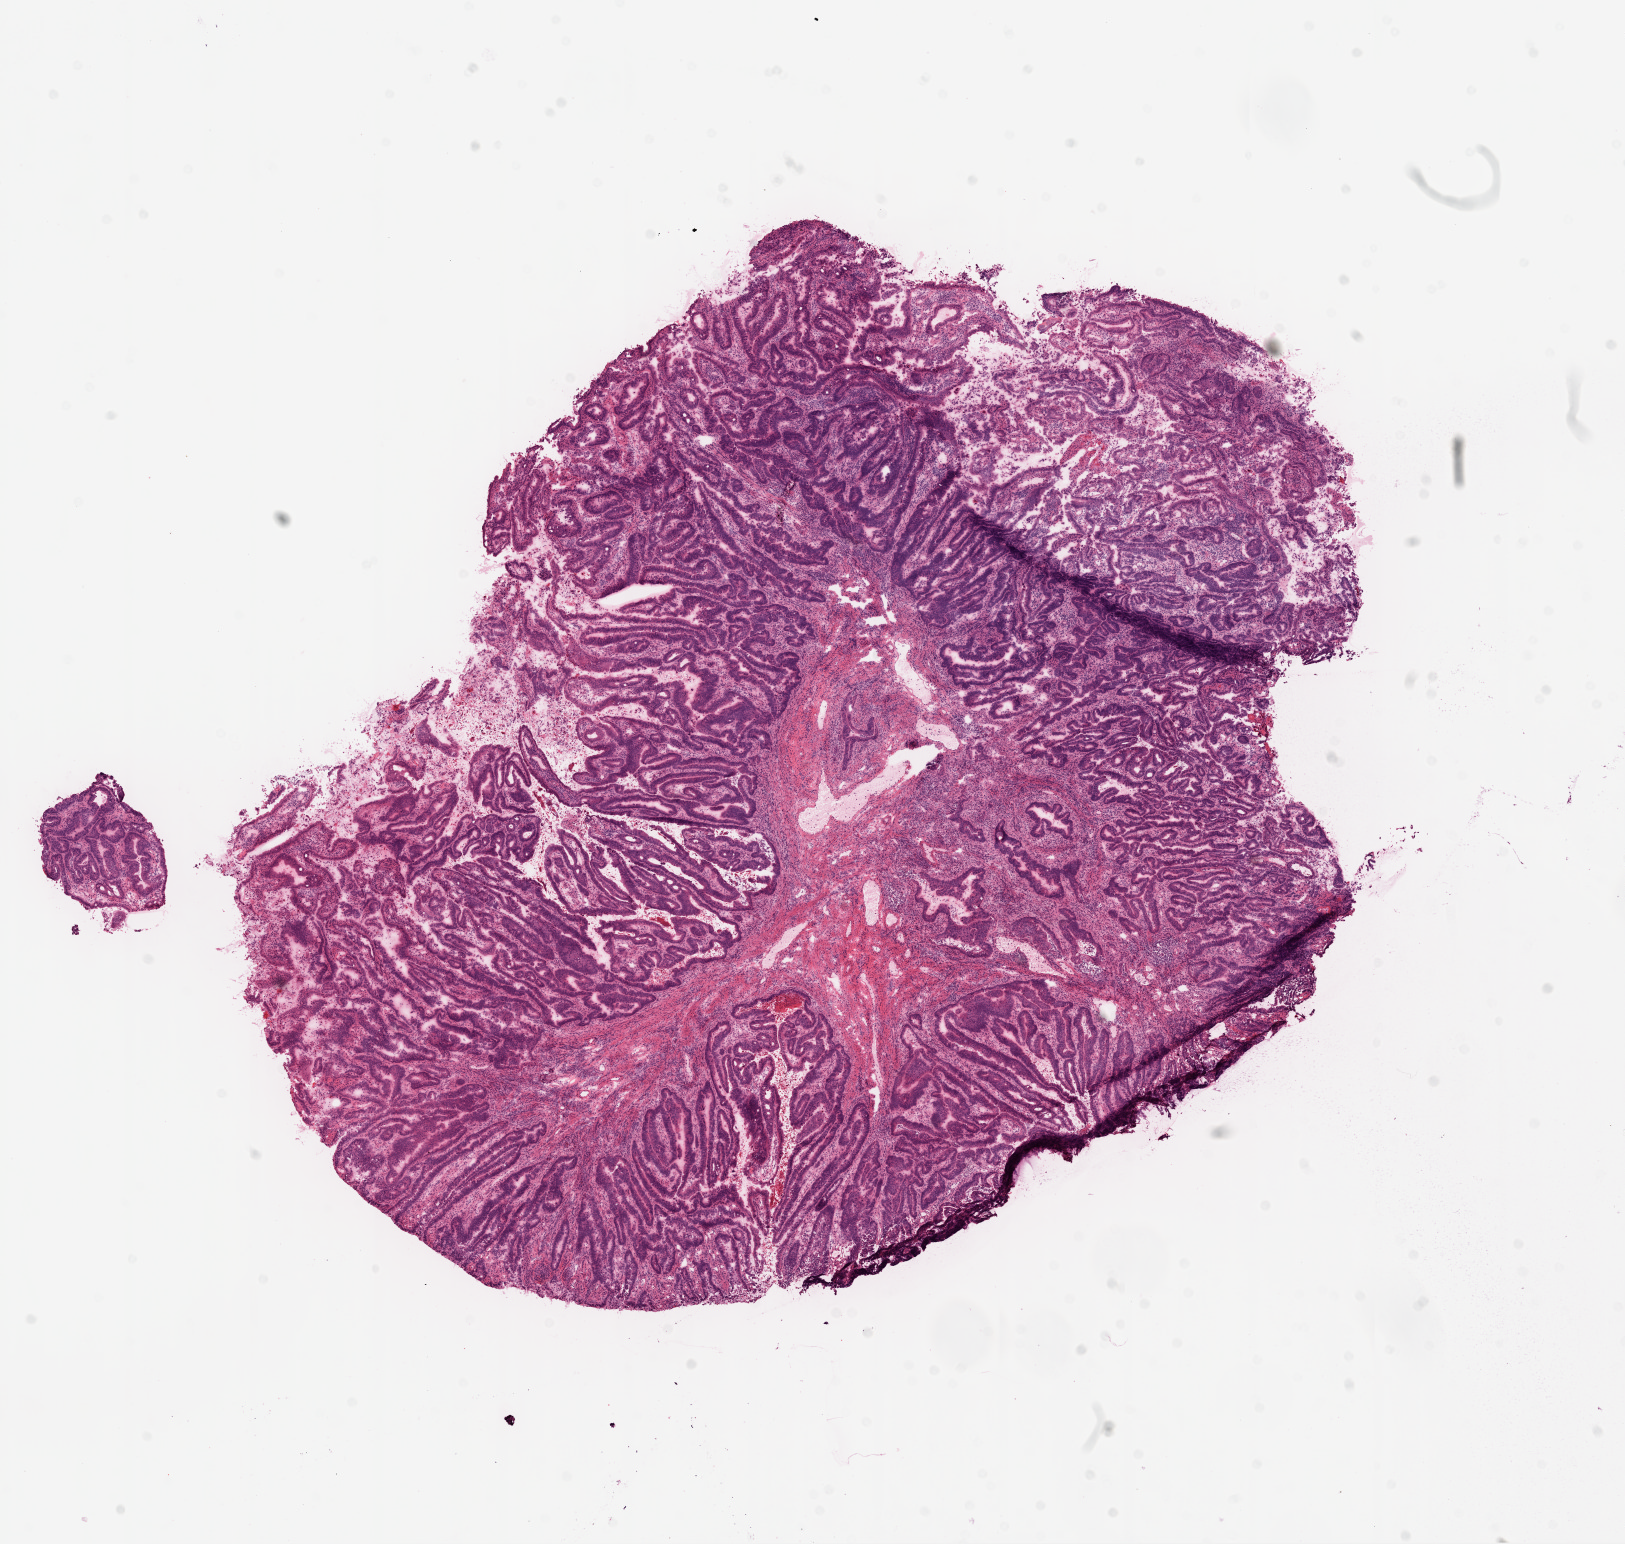
Whole-slide histology image, H&E, a low-resolution overview of the entire scanned area, about 13.0 x 12.4 mm (slide scanned at 20x). Frozen section from the top of the tissue portion. Rectum, primary tumour sample. Patient: male, age at initial diagnosis 68 years. Slide review estimates, as recorded: tumour cells 90%, tumour nuclei 80%, normal cells 0%, stromal cells 5%, necrosis 5%. Inflammatory infiltration, as recorded: lymphocyte infiltration 10%, monocyte infiltration 6%, neutrophil infiltration 2%.
- histologic diagnosis: Adenocarcinoma, NOS (rectosigmoid junction)
- AJCC pathologic stage: I (7th edition)
- TNM: T1 N0 M0